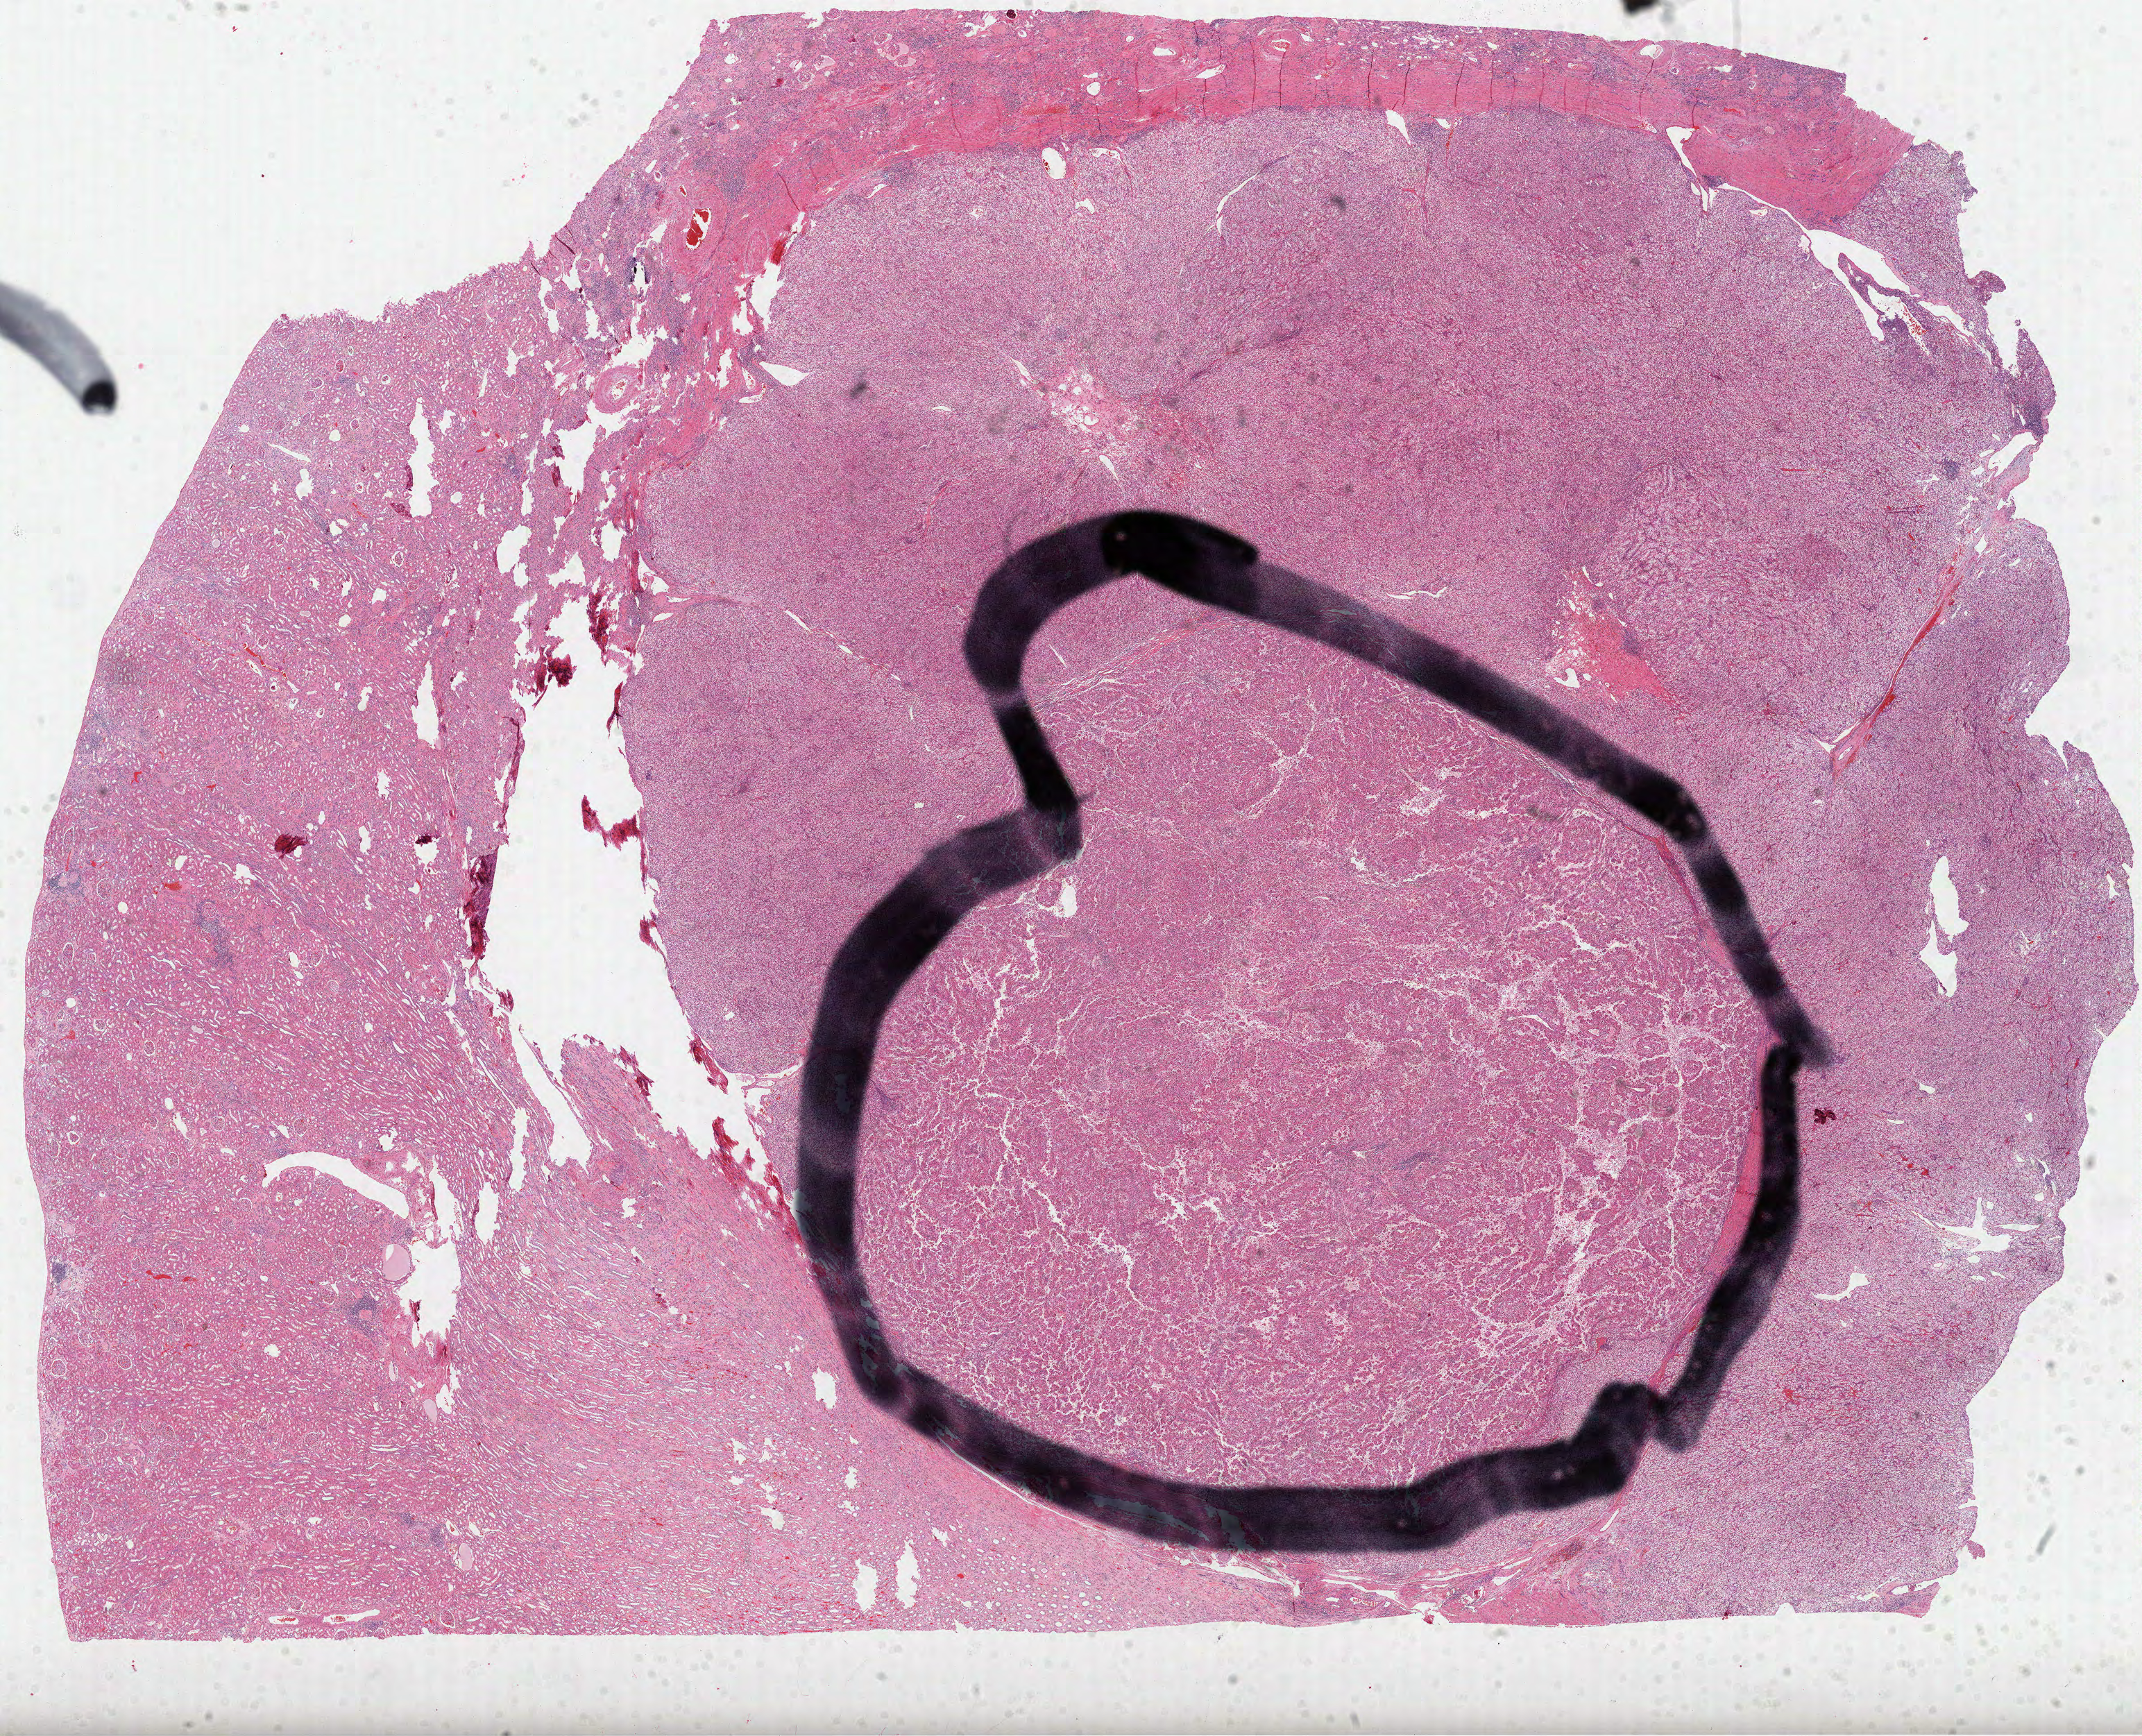
Whole-slide histology image, Hematoxylin and eosin (H&E) stained — low-resolution overview of the scanned area, about 24.9 x 20.2 mm (from a 40x scan); FFPE section; primary tumour sample from the kidney. Male patient; age at initial diagnosis 60 years. Histologic grade: G3 (poorly differentiated).
Laterality: left. Histologic diagnosis: Clear cell adenocarcinoma, NOS. AJCC pathologic stage: IV.